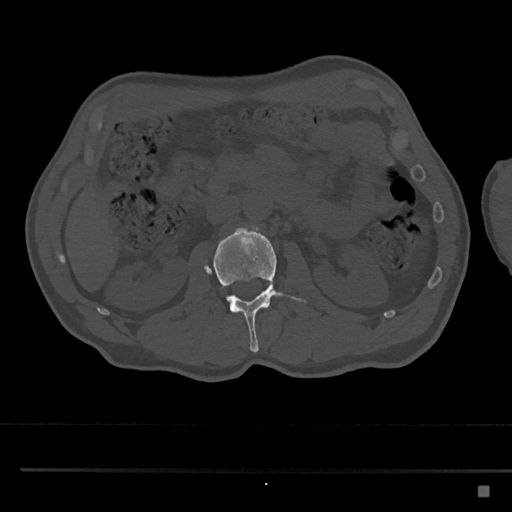
CT including the spine, one axial slice. Position 753 of 797 along the scan axis. 120 kVp. Bone window (W 1800 / L 400 HU). 0.5 mm slice thickness. 512 × 512 image matrix. Male patient, age 59 years. Case-level facts recorded for this patient, not image findings: primary cancer: prostate.
Outlined on this slice (semi-automatically segmented with operator editing):
- L2 vertebra: box from (x=204, y=226) to (x=306, y=352) px